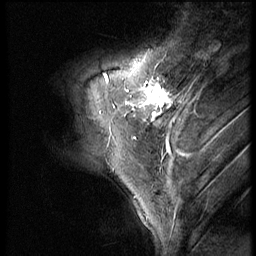
Breast MRI (dynamic contrast-enhanced), one sagittal slice. Position 14 of 56 along the scan axis. 3 images stored at this slice position (order not interpretable as contrast timing). 1.5 T. TE 4.2 ms, TR 9 ms. 2.5 mm slice thickness. 256 × 256 image matrix. Female patient, age 46 years. Case-level facts recorded for this patient, not image findings: setting: breast cancer imaged before/during neoadjuvant chemotherapy; receptor status: HER2-positive.
Annotated regions visible in this slice (semi-automatically segmented with operator editing):
- analysis volume of interest (the breast-tissue region the enhancement analysis was run in; not a lesion): bounding box (x1, y1, x2, y2) in pixels: (79, 68, 190, 143)
- tumour enhancement mask (voxels above the 140 % enhancement threshold inside the analysis volume of interest): (105, 76, 172, 120)